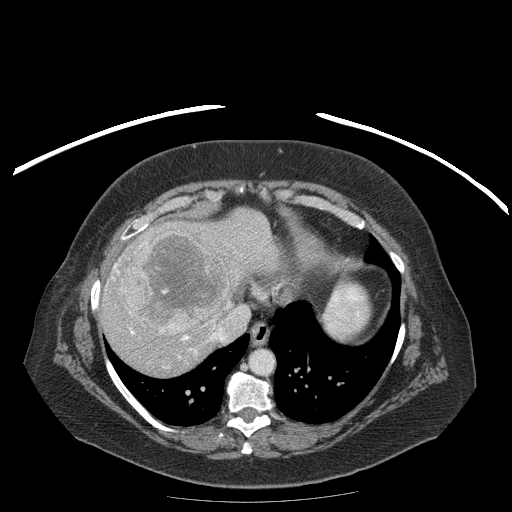
Contrast-enhanced abdominal CT (liver protocol), one axial slice; position 155 of 204 along the scan axis; 120 kVp; soft-tissue window (W 400 / L 40 HU); 2.5 mm slice thickness; 512 × 512 image matrix. From the clinical record (not read from this slice): diagnosis: hepatocellular carcinoma (patient treated with transarterial chemoembolisation; whether this scan precedes or follows treatment is not stated here); TNM stage (as recorded): Stage-IIIB; Child-Pugh class: A; tumour differentiation: well differentiated; tumour nodularity: uninodular.
Outlined on this slice (semi-automatic segmentation, software-assisted and operator-edited):
- liver parenchyma outside the tumour (the mass and vessels are separate outlines, so this box may not span the whole liver): bounding box <100,208,282,376> (left, top, right, bottom; pixels)
- mass: <125,232,228,335>
- liver vessels: <114,263,241,369>